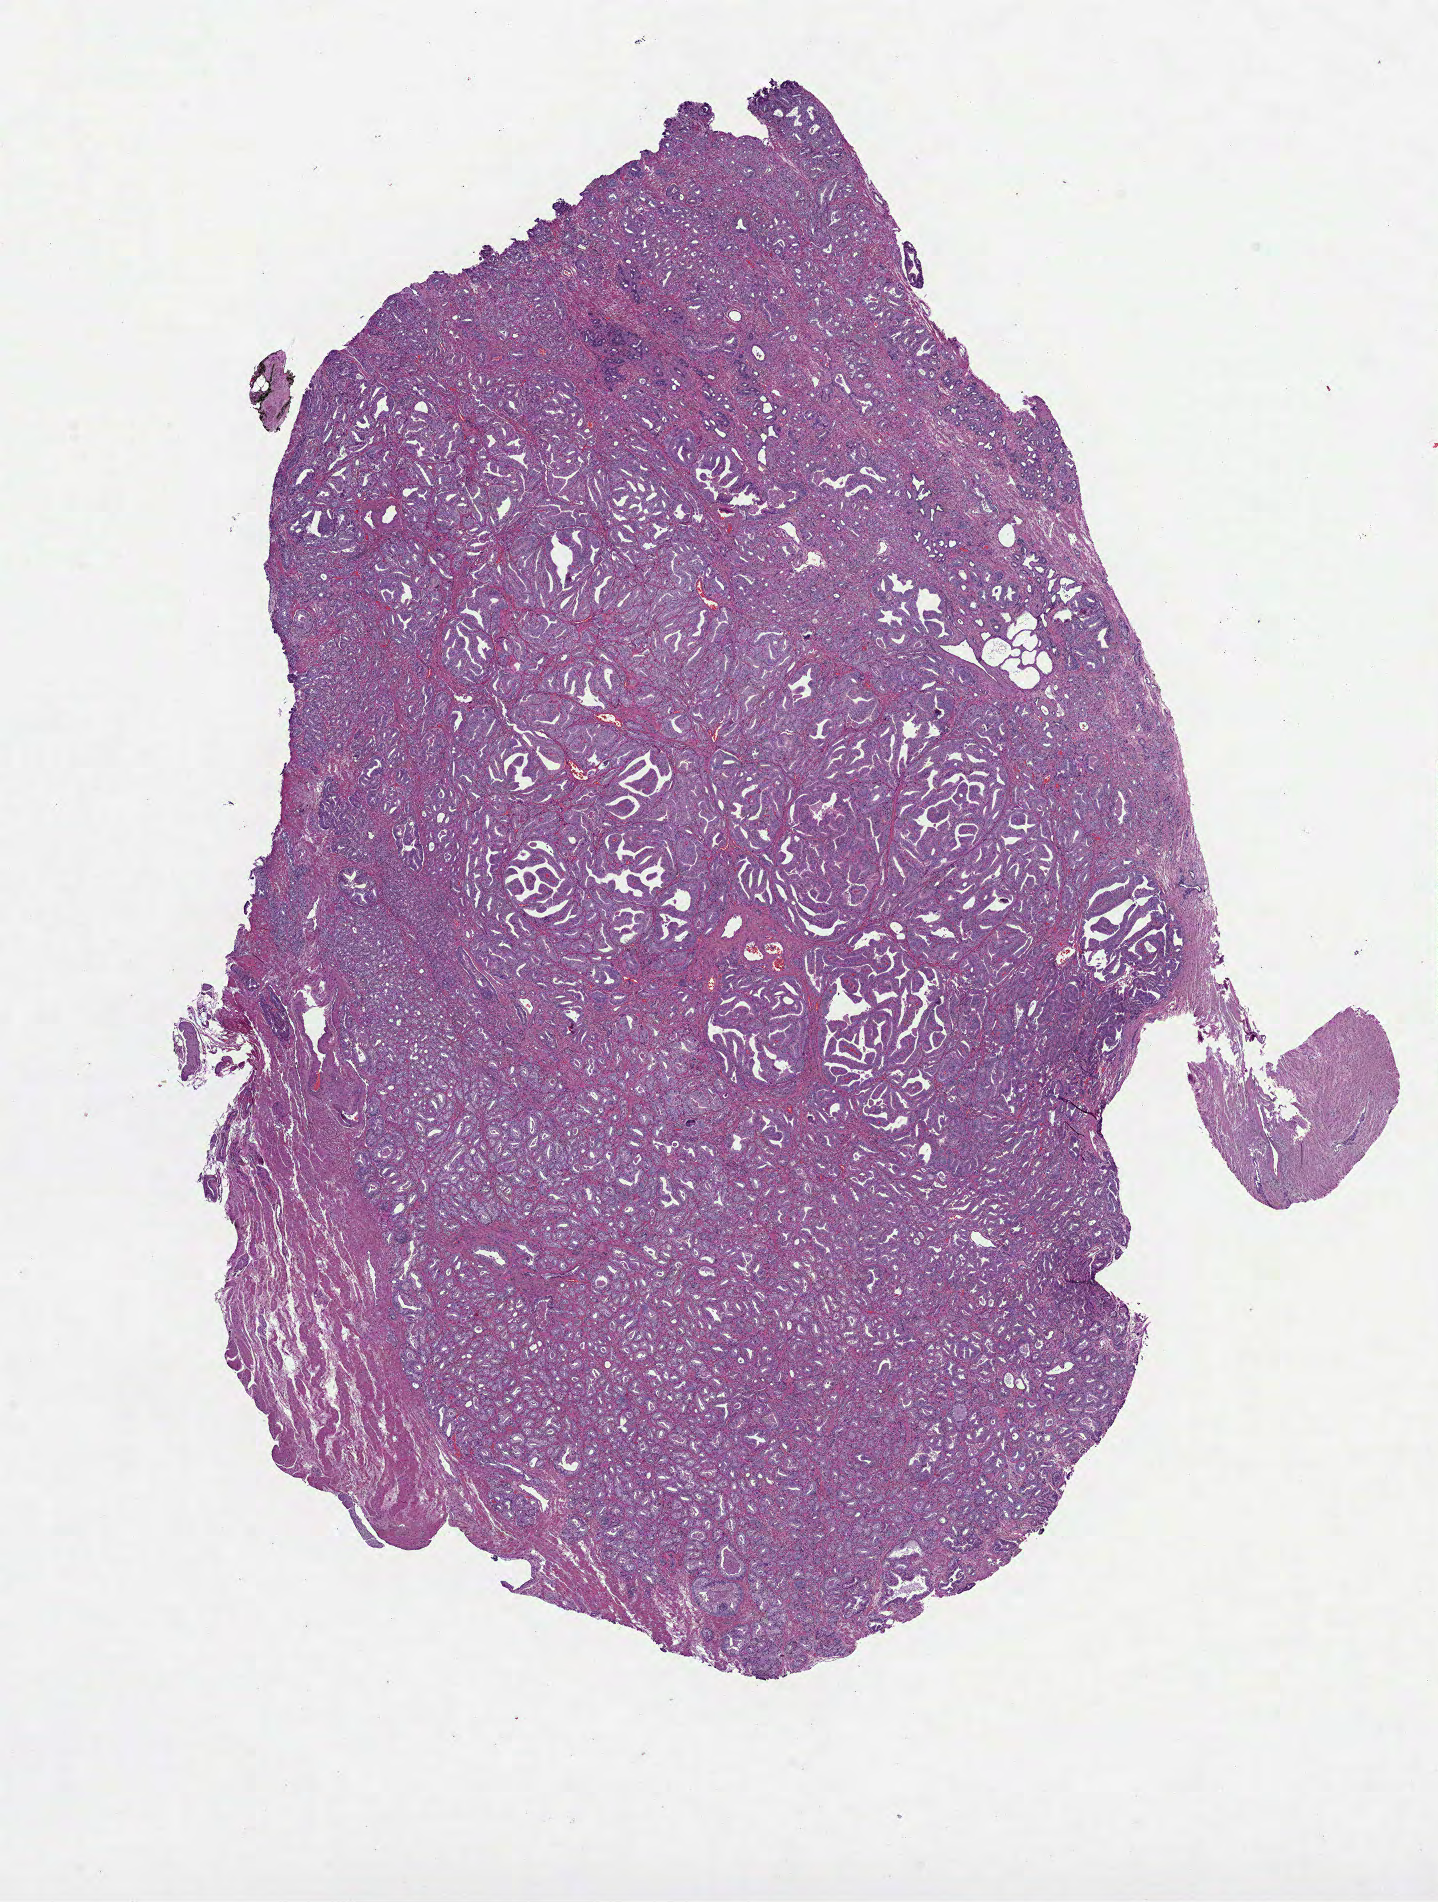
Whole-slide histology image, H&E, low-resolution overview of the scanned area, about 11.6 x 15.3 mm (slide scanned at 40x), FFPE section, primary tumour sample from the prostate. Patient: male, age at initial diagnosis 61 years. Gleason score: 7 (3+4).
Histologic diagnosis: Adenocarcinoma, NOS (prostate gland).